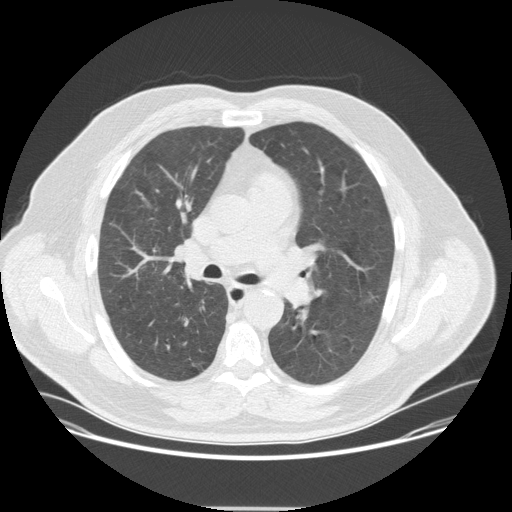
Low-dose screening chest CT, one axial slice; position 217 of 351 along the scan axis; reconstruction kernel STANDARD; 120 kVp; lung window (W 1500 / L -600 HU); 512 × 512 image matrix, field of view 419 × 419 mm.
Structures marked on this image (manually delineated by an expert):
- lesion 1 (tumor, upper lobe of right lung): bounding box [x1, y1, x2, y2] px = [184, 274, 193, 280]